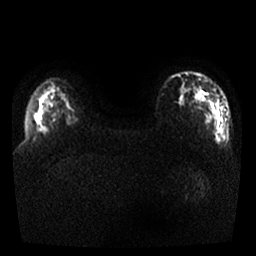
Breast MRI, one axial slice. Slice 4 of 25 in the series (ordered by position). Diffusion-weighted series; image 2 of 4 stored at this slice position (different b-values; order by instance number). 1.5 T. 4 mm slice thickness. 256 × 256 image matrix. Female patient.
Outlined on this slice (outlined manually by an expert reader):
- tumour on diffusion-weighted imaging: box from (x=193, y=86) to (x=223, y=145) px